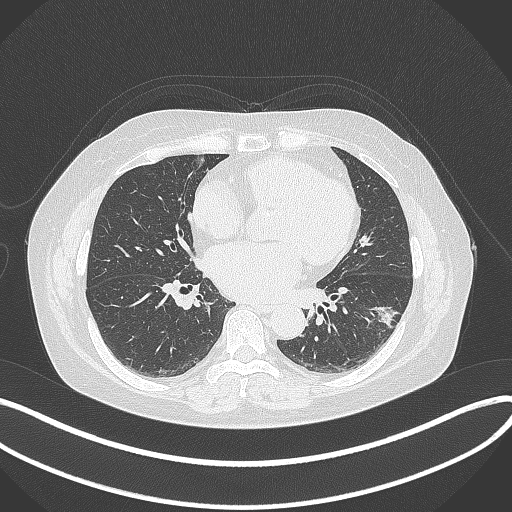
Chest CT, one axial slice; position 159 of 373 along the scan axis; lung window (W 1500 / L -600 HU); 1 mm slice thickness; 512 × 512 image matrix, field of view 400 × 400 mm. Patient: female, 67 years. From the clinical record (not read from this slice): clinical TNM (as recorded): T1c N0 M0; histopathological grade: G2.
Annotated regions visible in this slice (rectangle marked by the reading radiologist):
- lung tumour (recorded histology: adenocarcinoma): box from (x=365, y=300) to (x=401, y=334) px